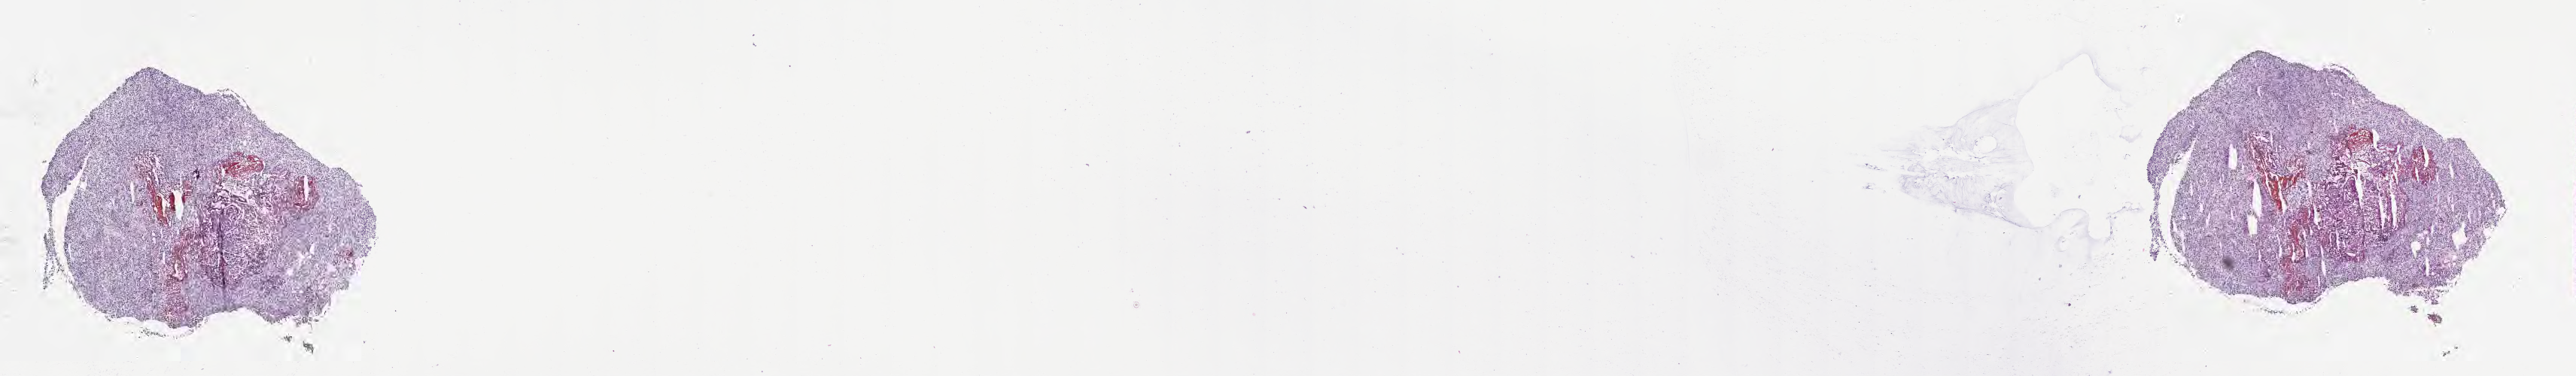
Whole-slide image, hematoxylin and eosin (H&E) stain of tumor tissue from the brain, shown as a low-resolution overview of the whole scanned area (about 27.7 x 4.0 mm), cryosection (OCT / tissue freezing medium). Patient male; age 79 months (6 years 7 months).
Diagnosis: Medulloblastoma, NOS.